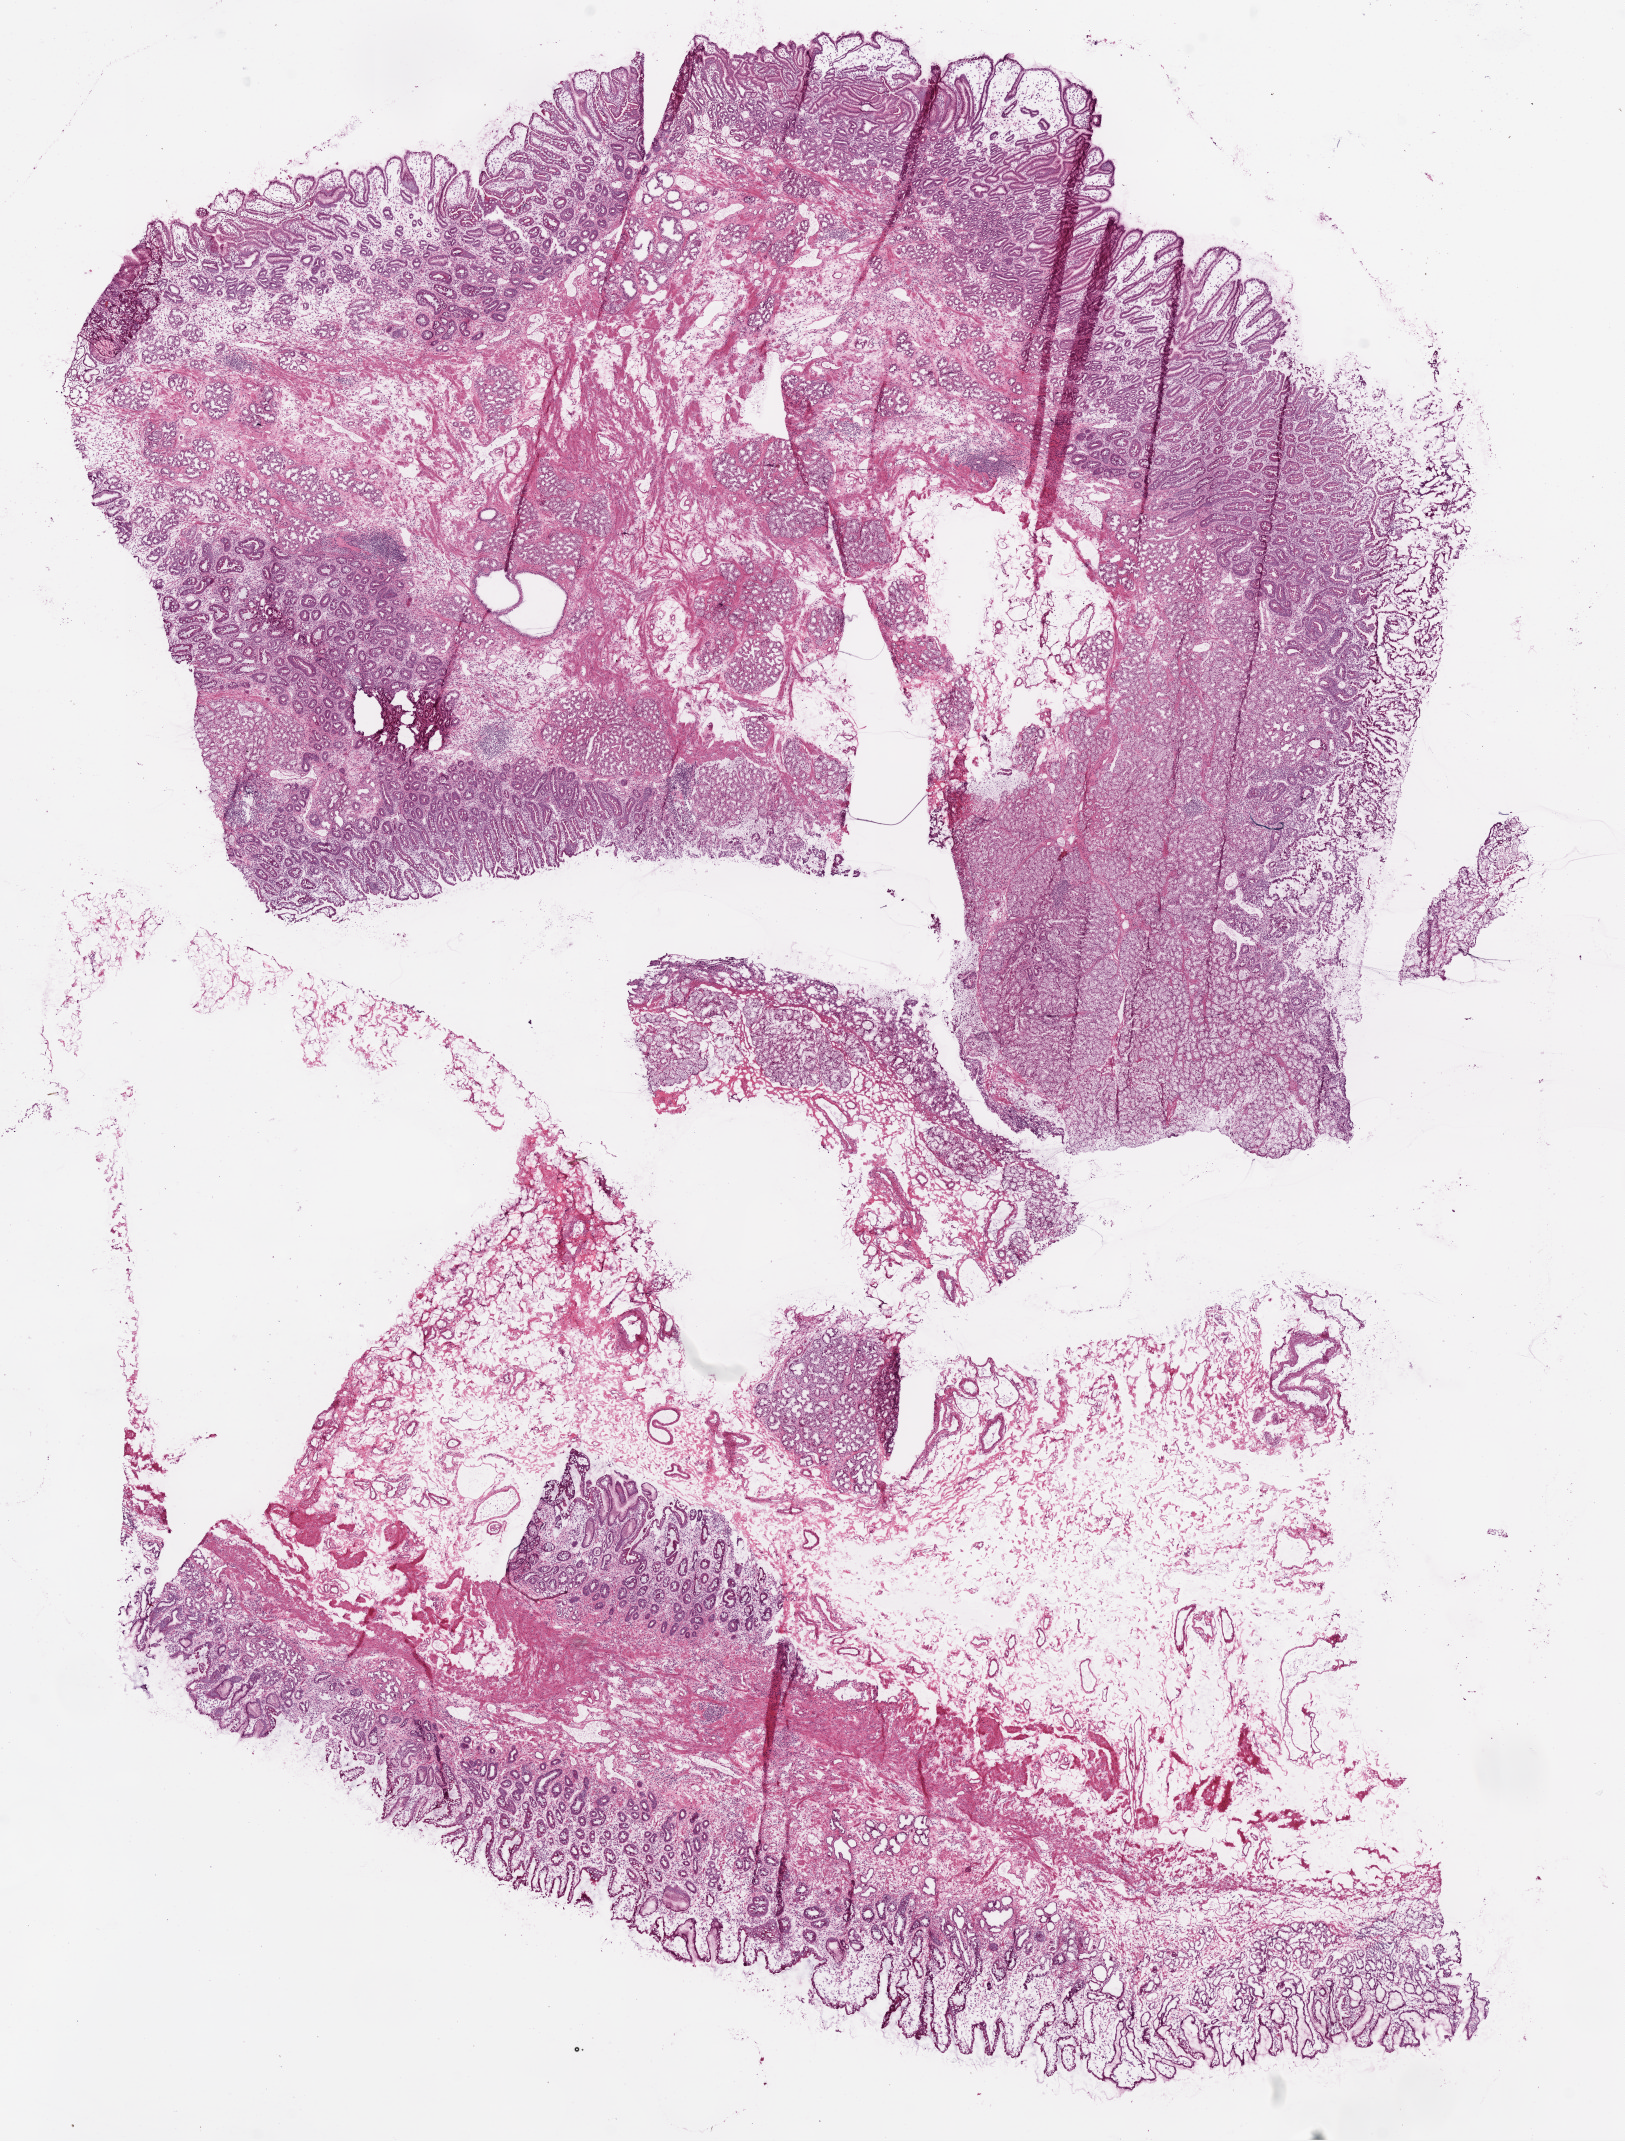
Digitized H&E-stained tissue section (whole slide), whole scanned area (about 13.0 x 17.2 mm, from a 20x scan) shown as a low-resolution overview; frozen section from the bottom of the tissue portion; stomach, solid tissue normal (non-tumour tissue) sample. Patient: female, age at initial diagnosis 76 years.
• this section: solid tissue normal (non-tumour) sample from the same patient
• patient diagnosis: Adenocarcinoma, NOS